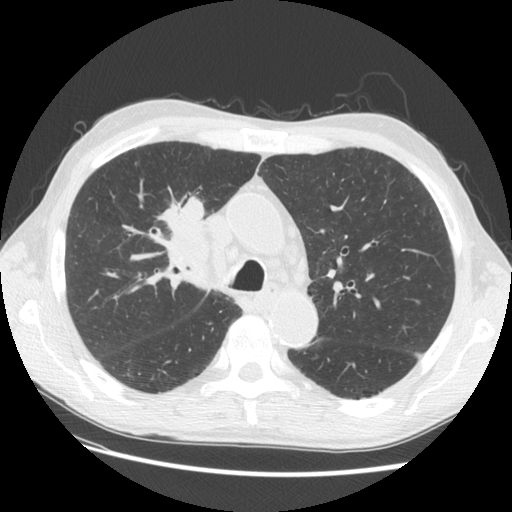
Low-dose screening chest CT, one axial slice; slice 91 of 133 in the series (ordered by position); reconstruction kernel STANDARD; lung window (W 1500 / L -600 HU); 2.5 mm slice thickness; 512 × 512 image matrix, field of view 360 × 360 mm.
Structures marked on this image (outlined manually by an expert reader):
- lesion 1 (tumor, hilum of right lung): bounding box (x1, y1, x2, y2) in pixels: (157, 191, 211, 268)